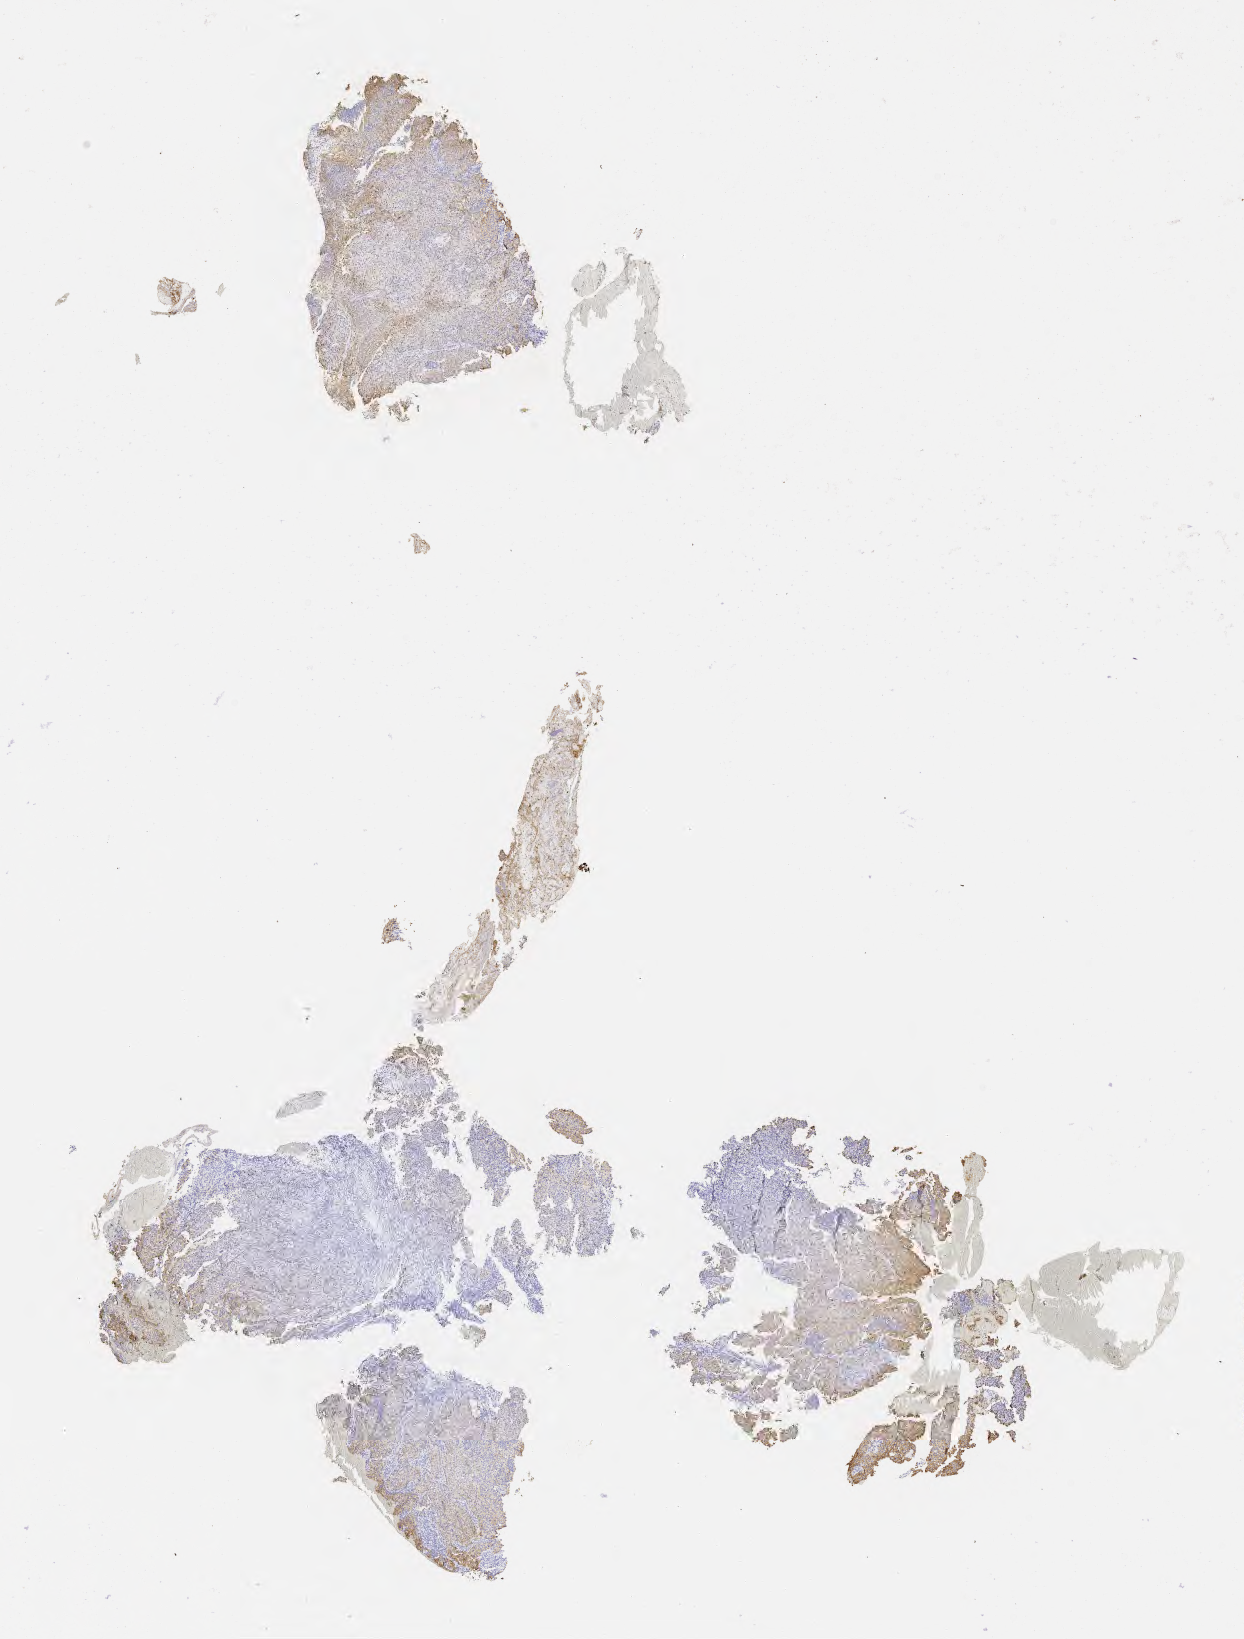
Whole-slide image, immunohistochemical stain for MOC-31 (anti-EpCAM) — whole scanned area (about 10.1 x 13.3 mm) shown as a low-resolution overview, tumor tissue, anatomic site: cervix. Female patient, age 33 years.
Histologic diagnosis: Squamous cell carcinoma, large cell, nonkeratinizing, NOS.